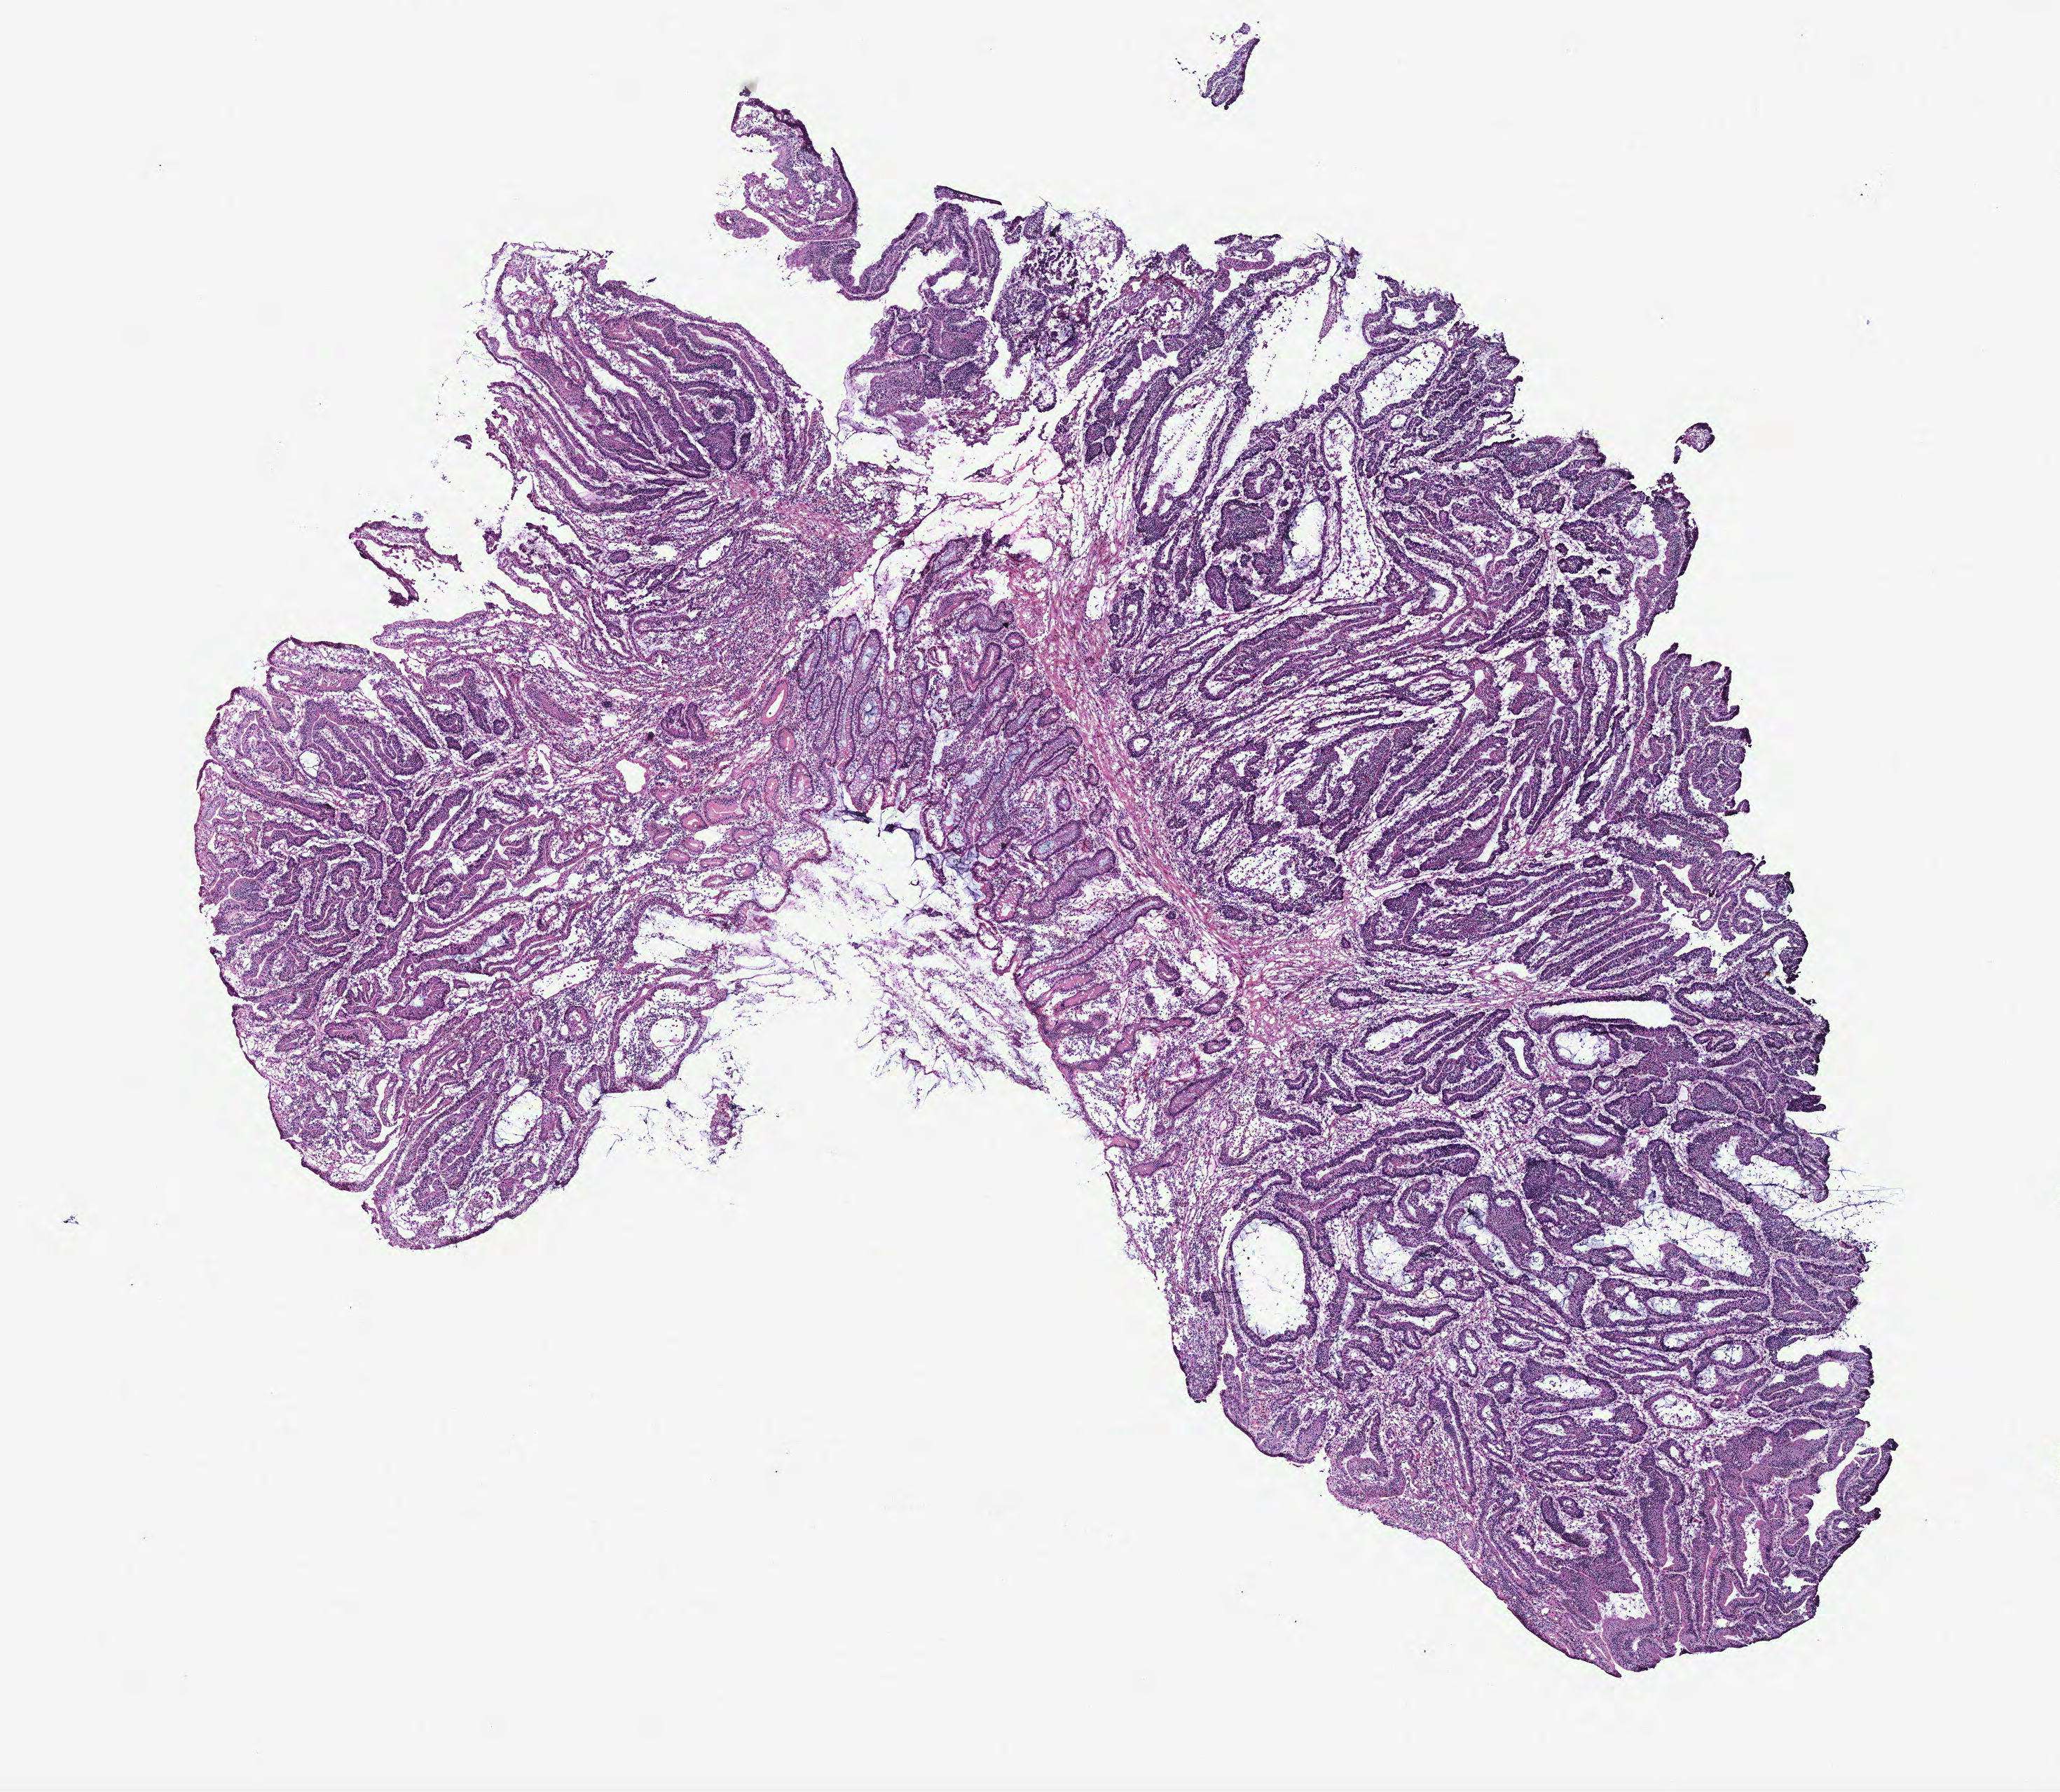
Digitized H&E-stained tissue section (whole slide), shown as a low-resolution overview of the whole scanned area (about 11.8 x 10.2 mm, slide scanned at 40x). Colon, tumour tissue. 73-year-old male patient.
Primary tumour site (as recorded): colon. Diagnosis: Adenocarcinoma, NOS. AJCC pathologic stage: IIB.